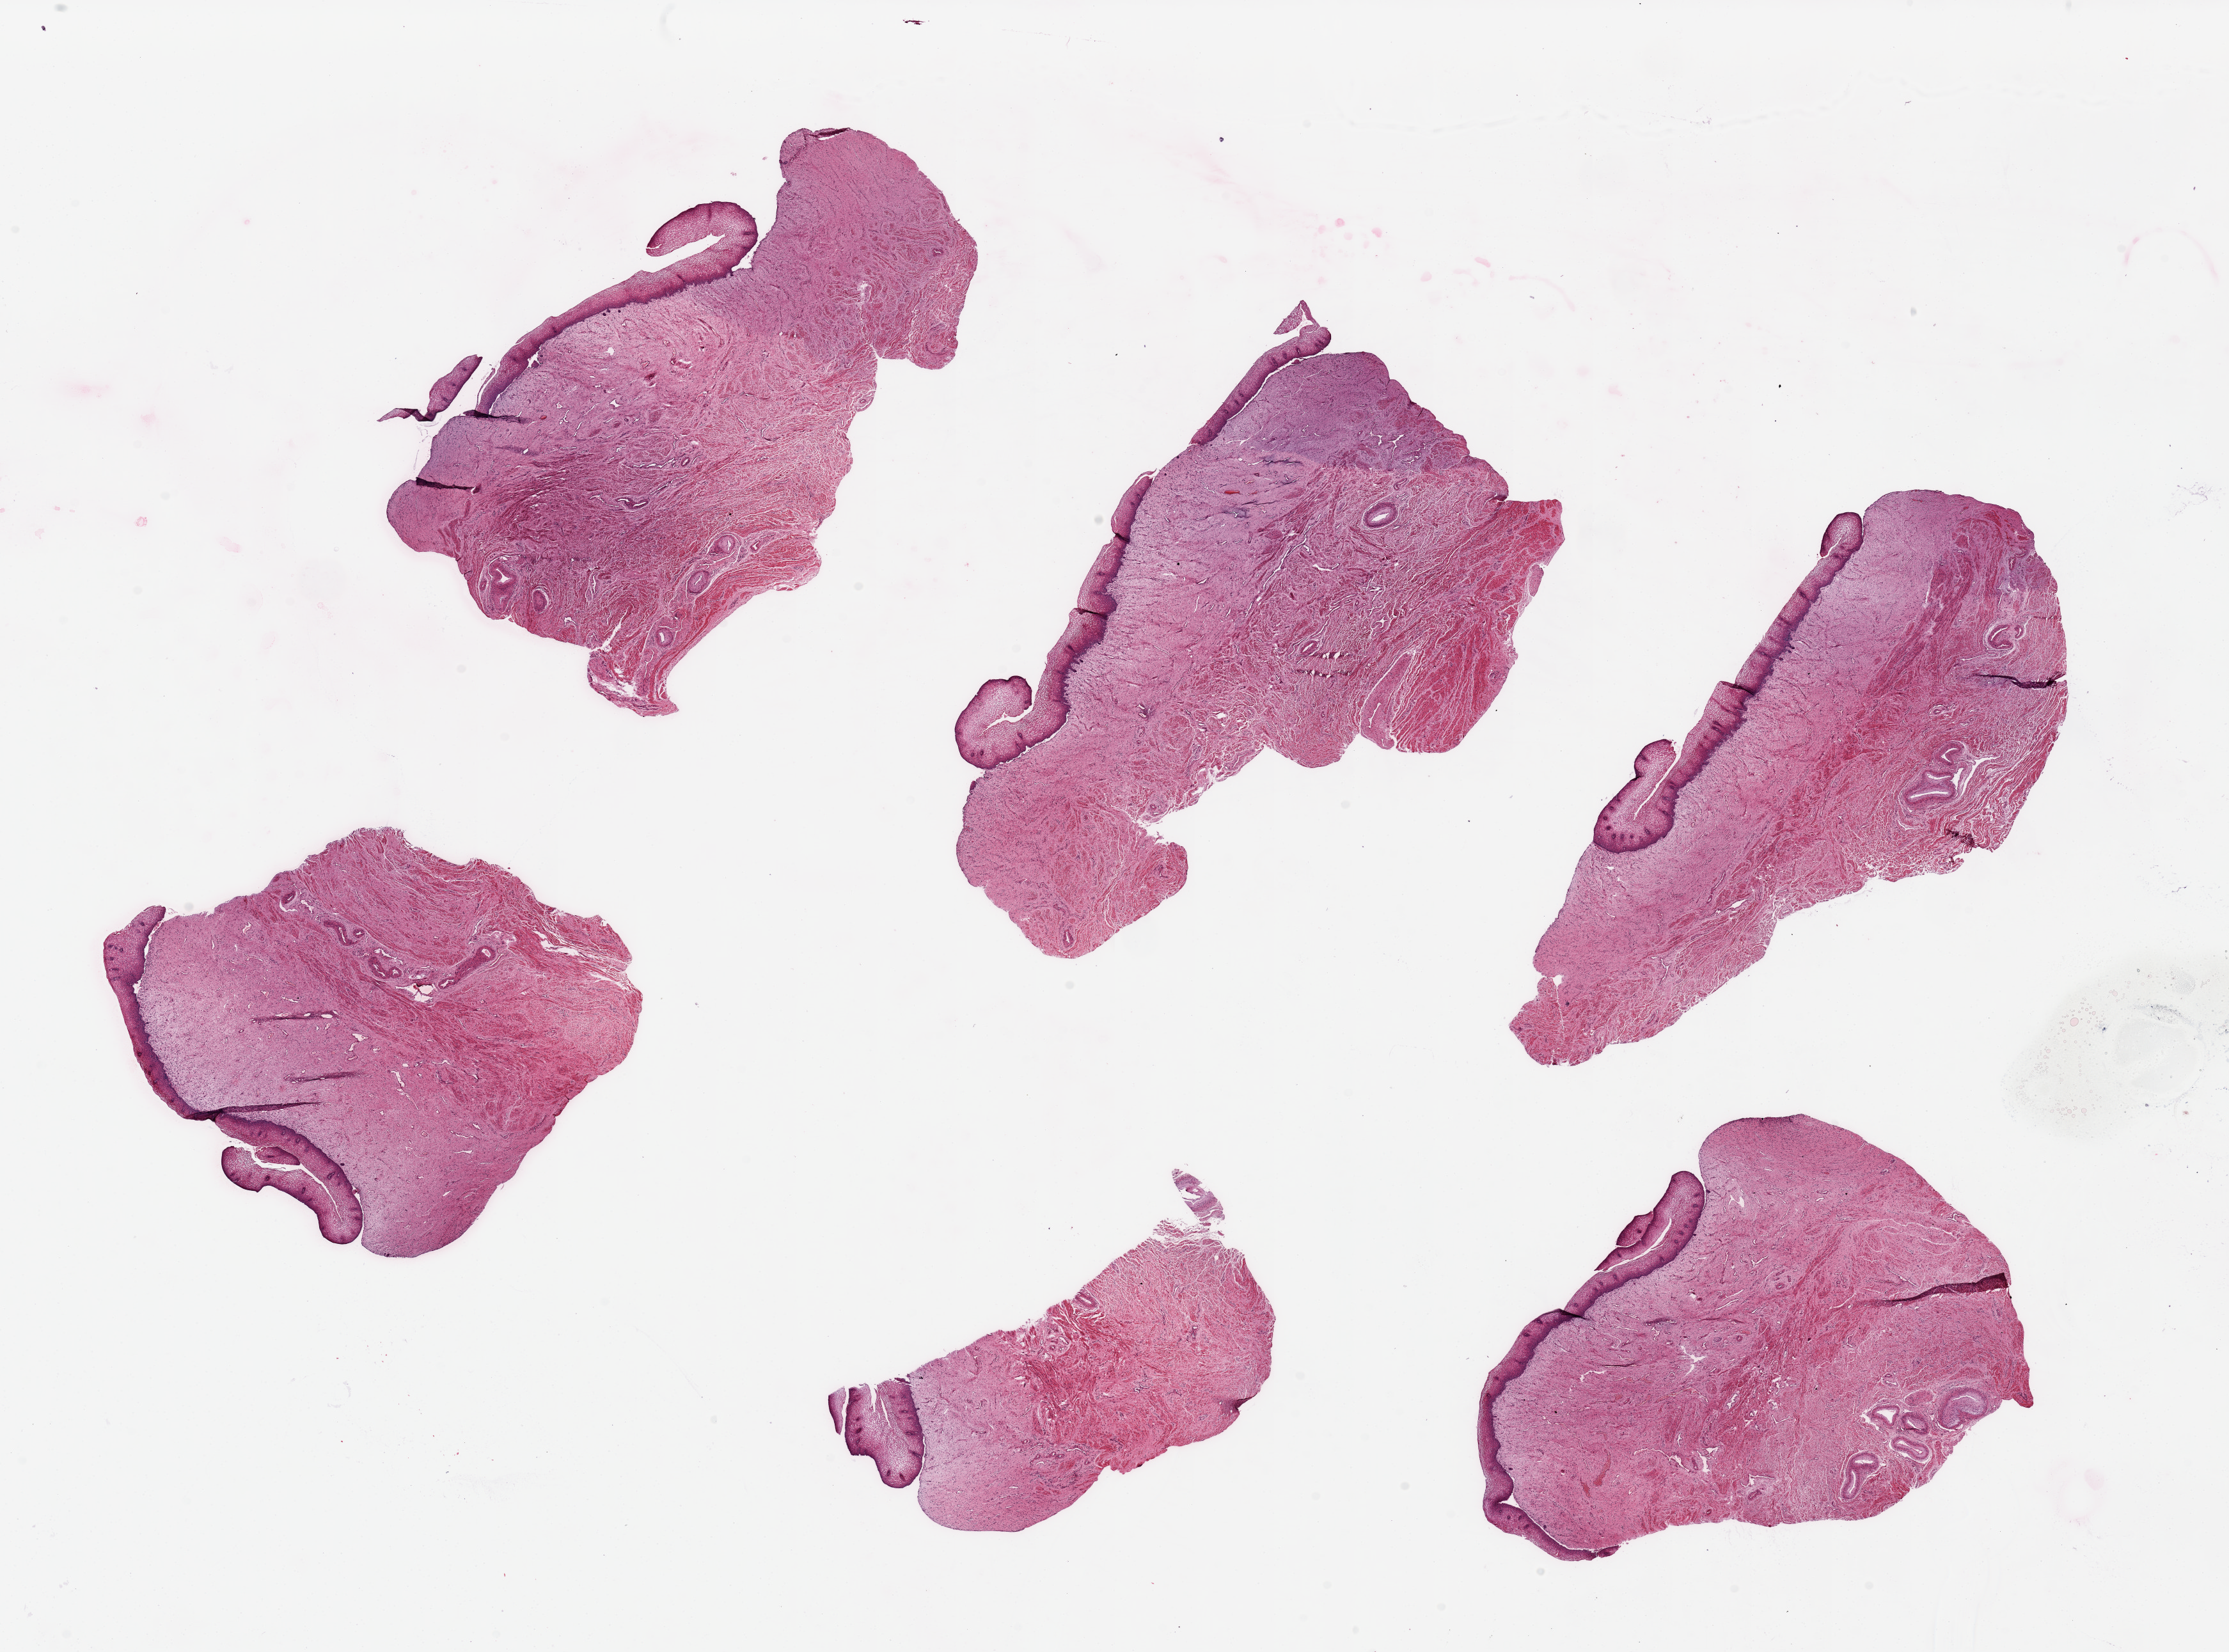
Whole-slide image, hematoxylin and eosin (H&E) stain — whole scanned area (about 27.6 x 20.4 mm, acquisition: 20x scan) shown as a low-resolution overview, PAXgene-fixed, paraffin-embedded tissue, section of vagina (target tissue), donor tissue sample. Donor: female.
Reviewer comment on this tissue sample: 6 pieces, up to 9x4mm; good specimen.